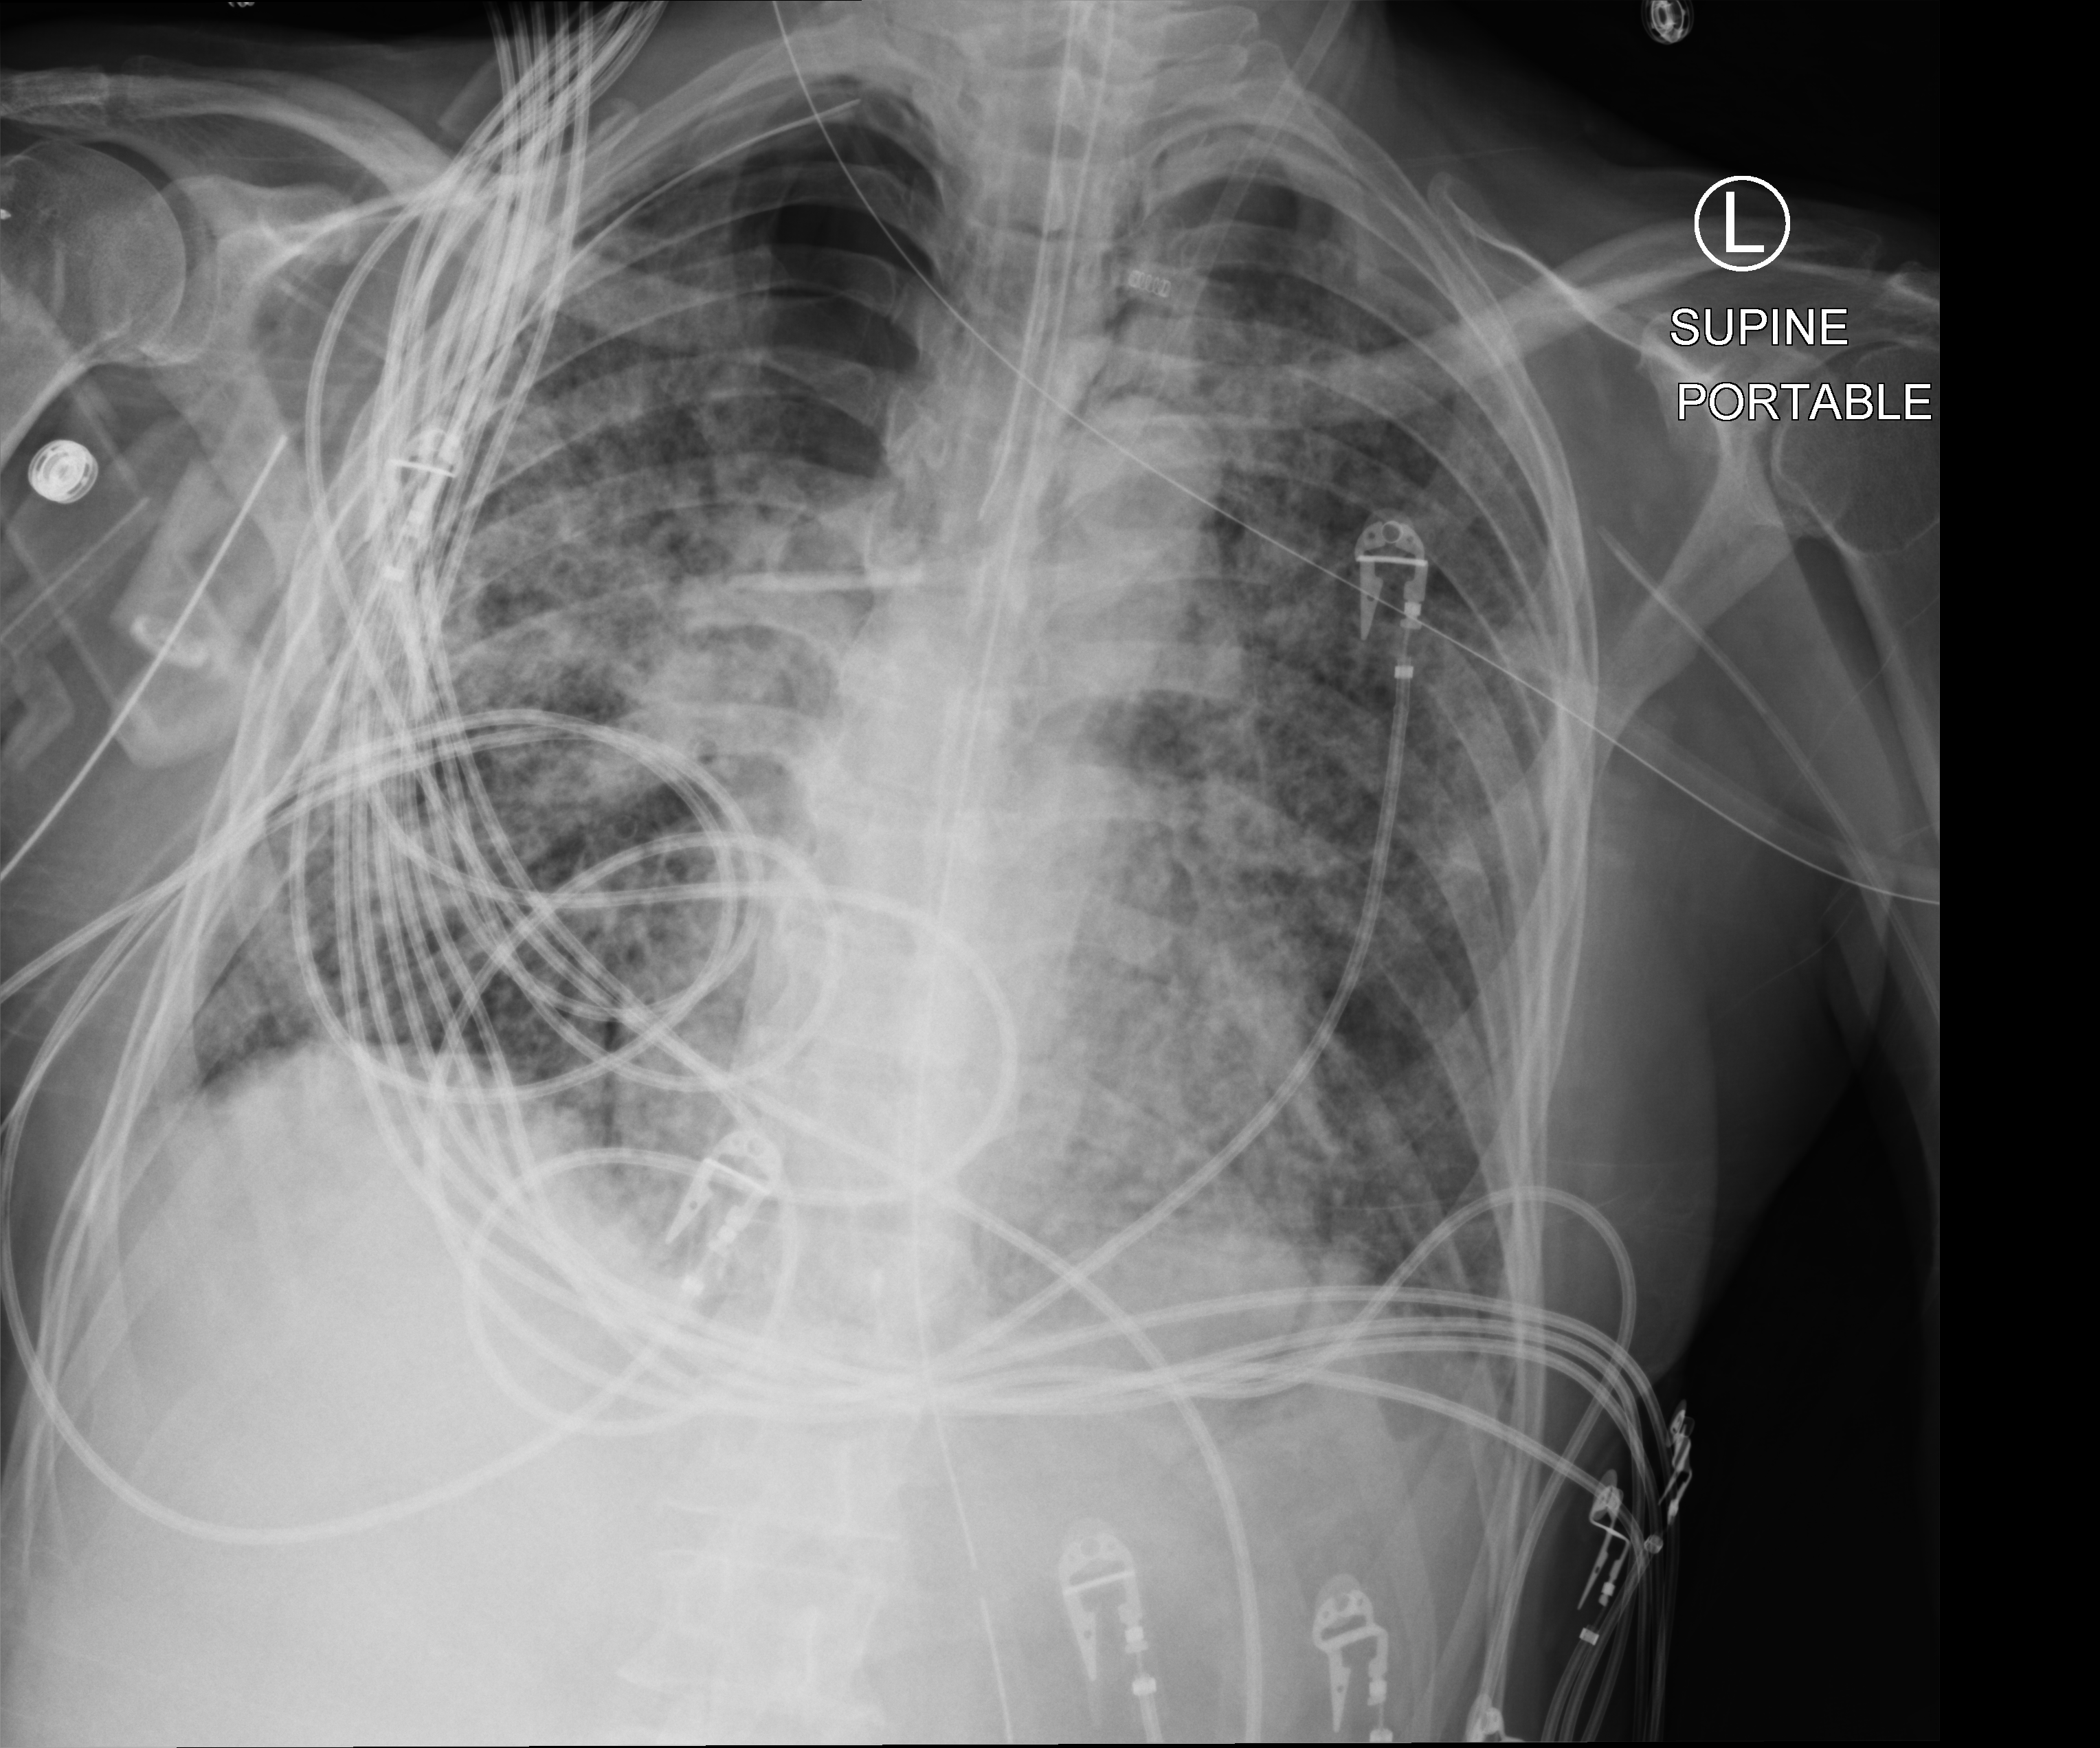
Portable chest radiograph; anteroposterior (AP) projection. Male patient hospitalised with COVID-19, age 60–74 years.
Admission-level facts for this patient (not findings on this image; timing relative to this image not recorded):
- admitted to intensive care during this hospital stay: yes
- mechanically ventilated during this hospital stay: yes